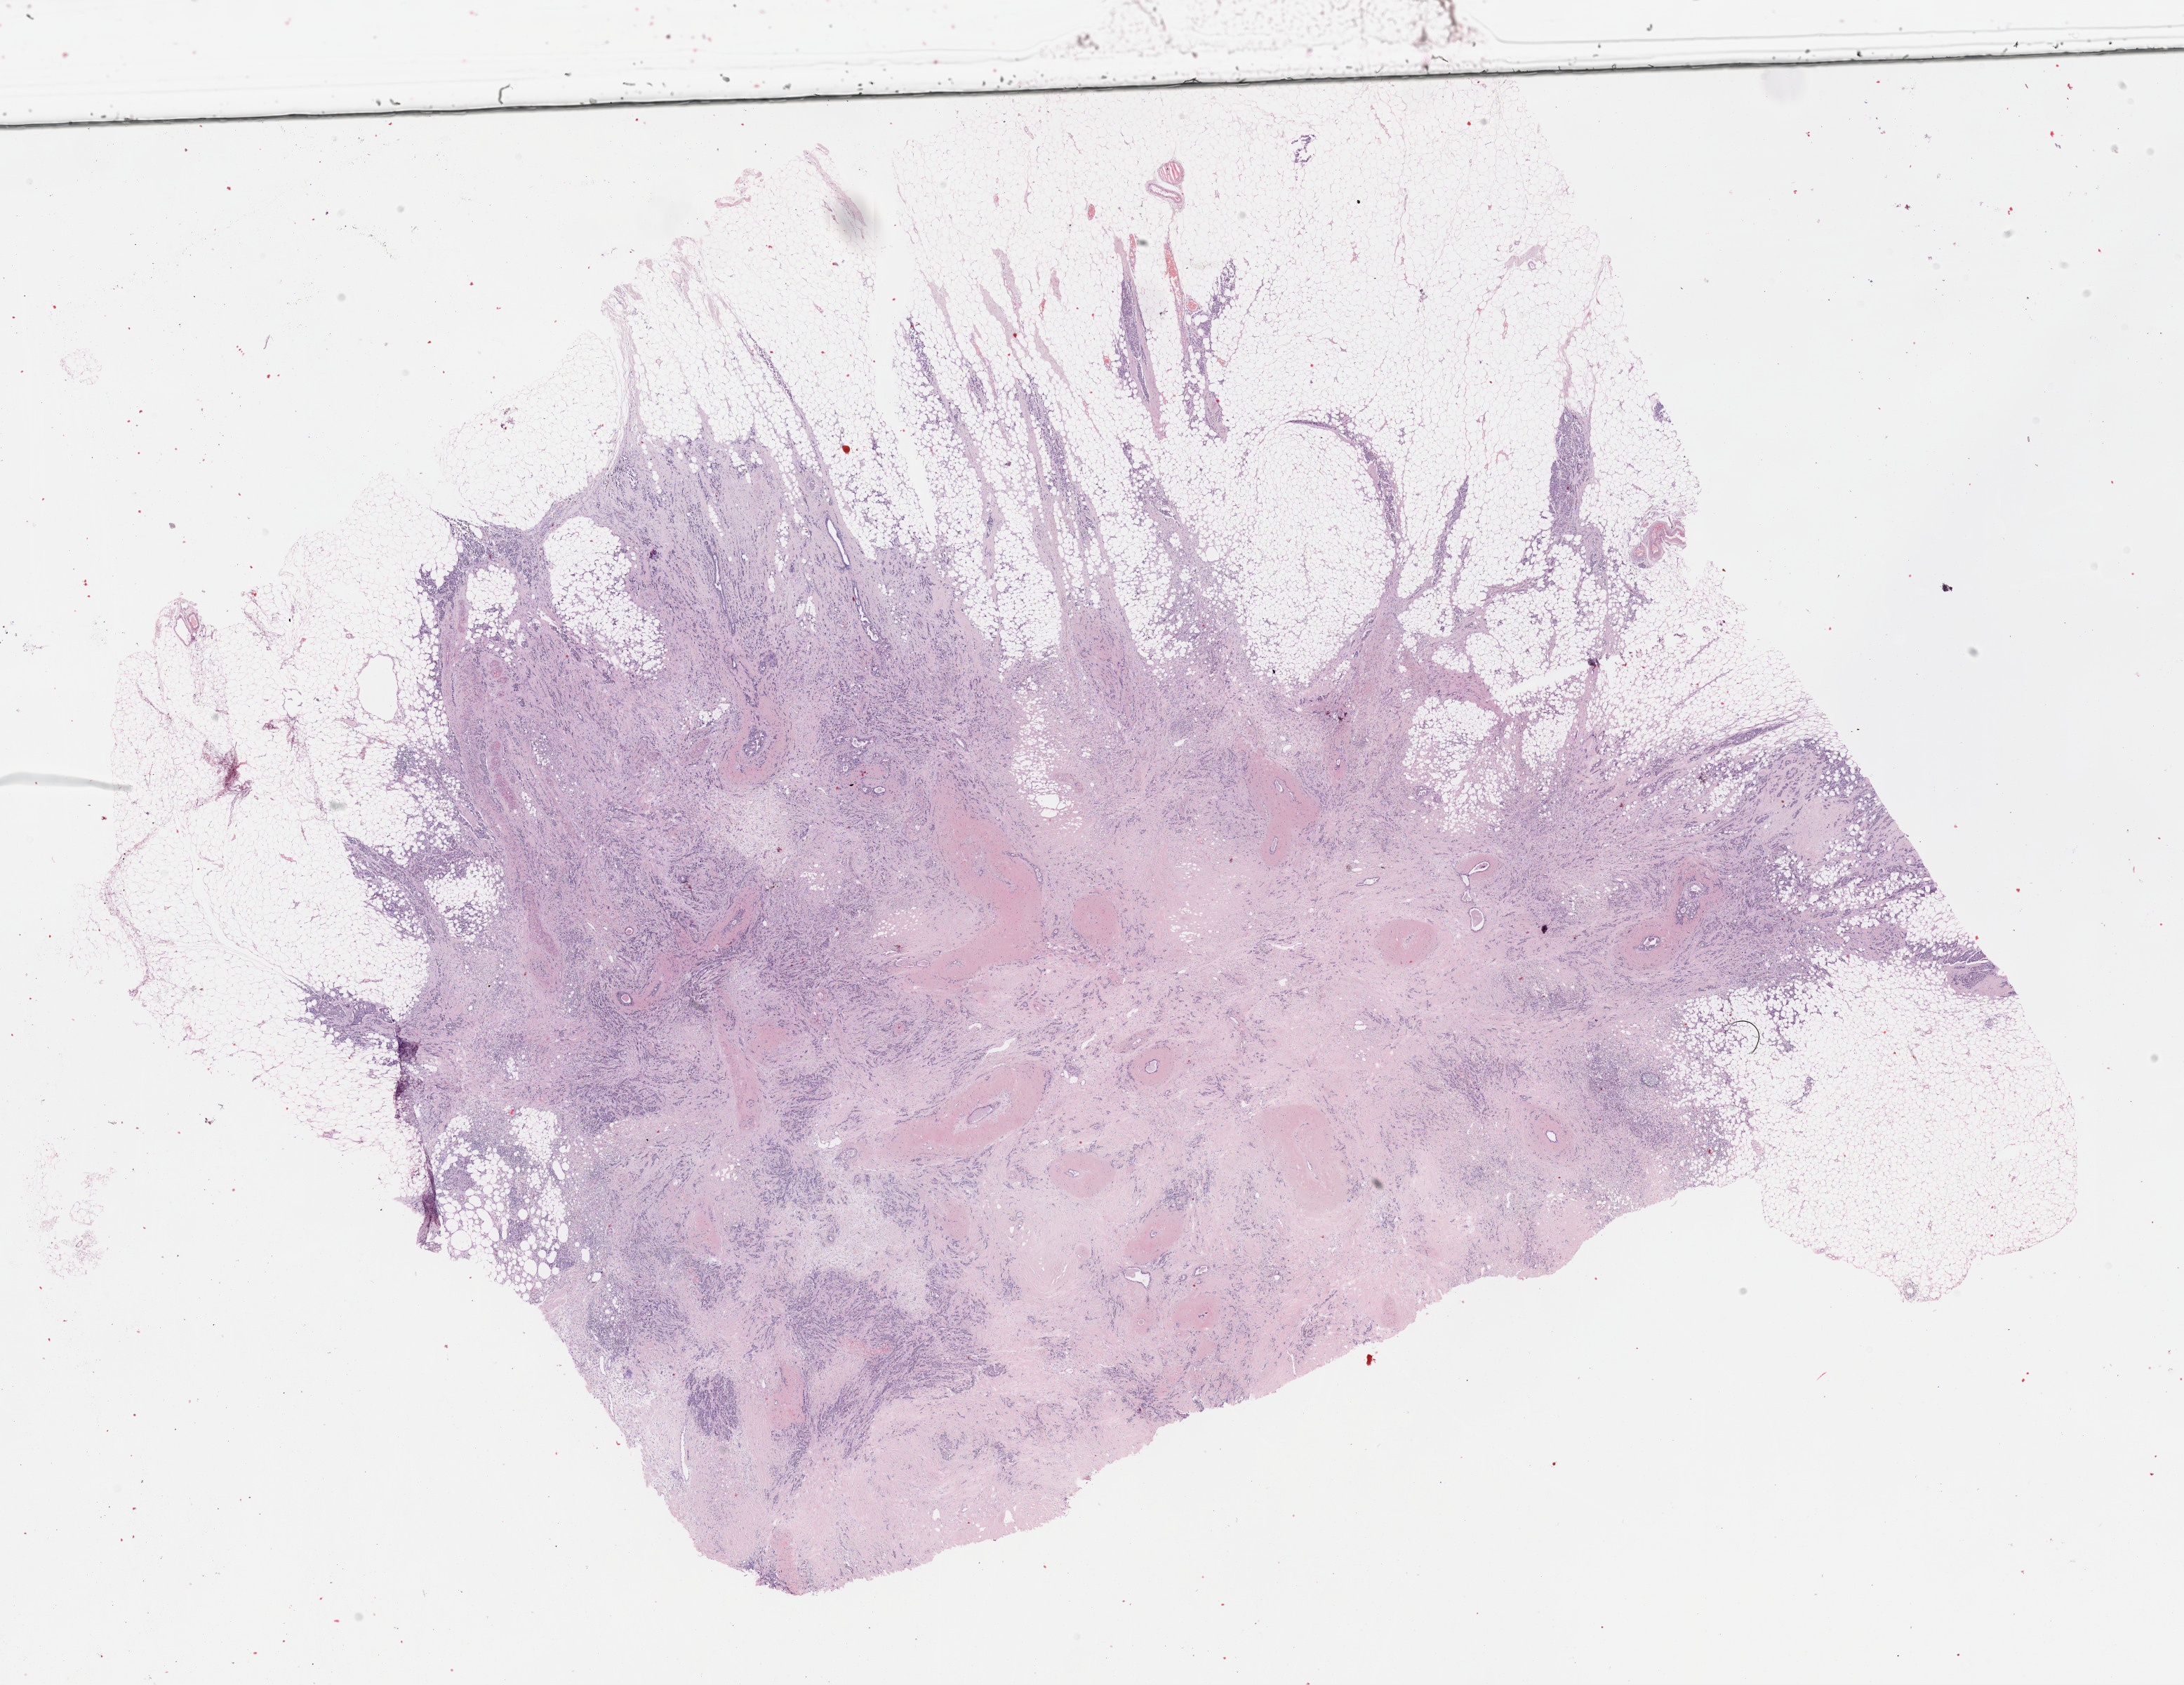
Whole-slide histology image, Hematoxylin and eosin (H&E) stained, shown as a low-resolution overview of the whole scanned area (about 25.2 x 19.4 mm), formalin-fixed paraffin-embedded (FFPE) diagnostic section, breast, primary tumour sample. Female patient; age at initial diagnosis 71 years.
Lymph nodes positive (case pathology): 0 of 7 examined. Laterality: right. Pathologic diagnosis: Infiltrating duct carcinoma, NOS. AJCC pathologic stage: IIA (7th edition).